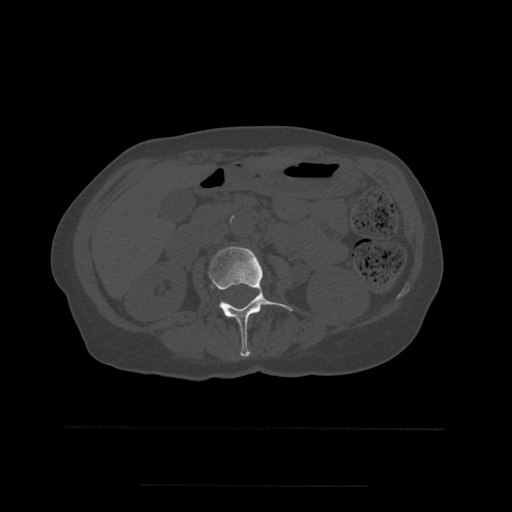
CT including the spine, one axial slice. Position 209 of 544 along the scan axis. Bone window (W 1800 / L 400 HU). 512 × 512 image matrix, field of view 350 × 350 mm. Patient age 58 years. Case-level facts recorded for this patient, not image findings: primary cancer: lung.
Structures marked on this image (semi-automatic segmentation, software-assisted and operator-edited):
- L2 vertebra: bounding box <207,247,293,357> (left, top, right, bottom; pixels)